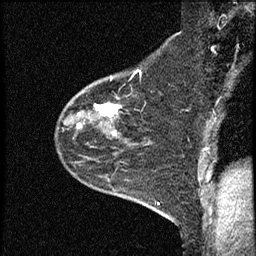
Breast MRI (dynamic contrast-enhanced), one sagittal slice; slice 47 of 60 in the series (ordered by position); dynamic contrast-enhanced study with each time point stored as its own series, time point 2 of 4 at this slice position (early post-contrast, ordered by acquisition time); 1.5 T; TE 4.2 ms, TR 17.6 ms; 256 × 256 image matrix, field of view 200 × 200 mm. Female patient, age 53 years. From the clinical record (not read from this slice): setting: breast cancer imaged before/during neoadjuvant chemotherapy; receptor status: HR-positive, HER2-negative.
Structures marked on this image (semi-automatic segmentation, software-assisted and operator-edited):
- analysis volume of interest (the breast-tissue region the enhancement analysis was run in; not a lesion): bounding box <55,69,154,199> (left, top, right, bottom; pixels)
- tumour enhancement mask (voxels above the 100 % enhancement threshold inside the analysis volume of interest): <77,104,121,135>